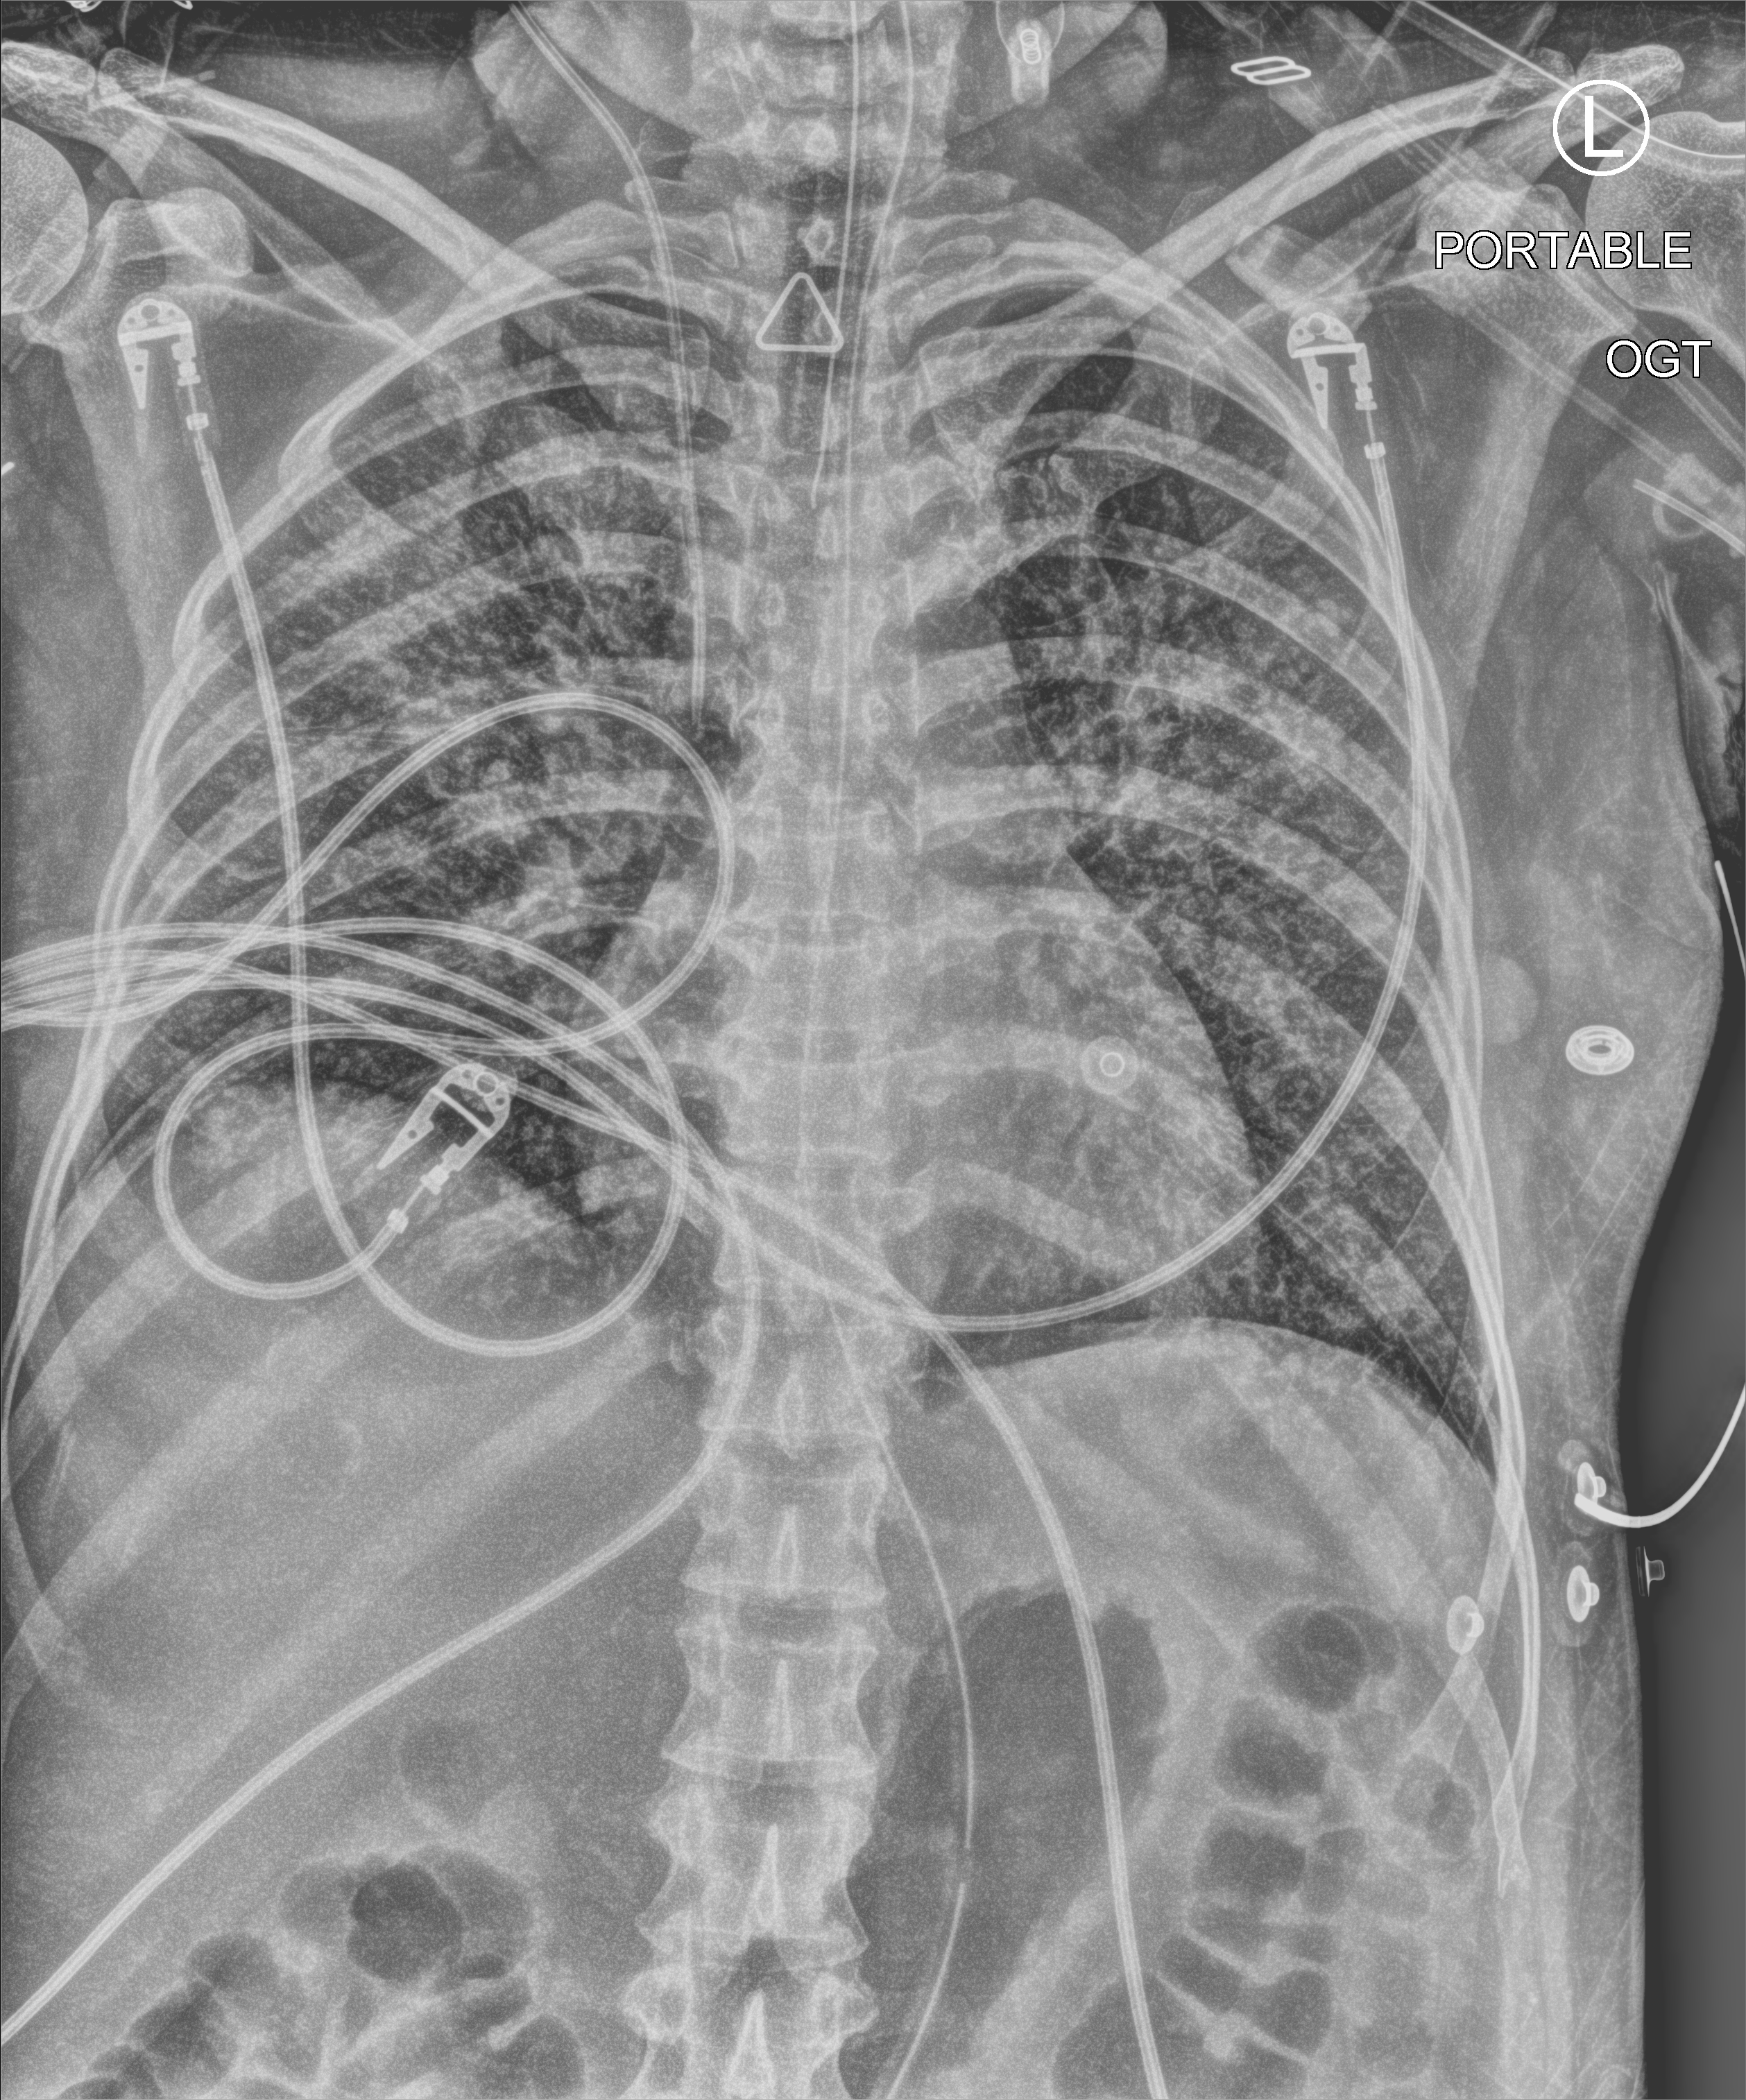
Chest X-ray (portable), anteroposterior (AP) projection. Female patient hospitalised with COVID-19, age 18–59 years.
From the hospital-stay record, not from the radiograph (when in the stay this image was taken is not recorded): mechanically ventilated during this hospital stay: yes; admitted to intensive care during this hospital stay: yes.